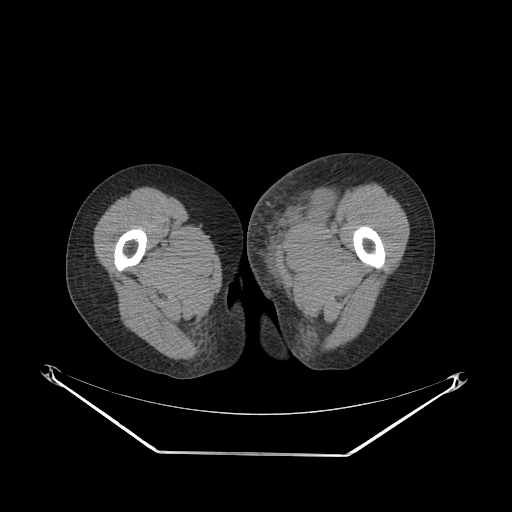
CT of an extremity soft-tissue mass (from a PET/CT study), one axial slice; slice 45 of 267 in the series (ordered by position); 140 kVp; soft-tissue window (W 400 / L 40 HU); 3.75 mm slice thickness; 512 × 512 image matrix, field of view 500 × 500 mm. Female patient. Case-level facts recorded for this patient, not image findings: histological type: leiomyosarcoma; grade: high; site of the primary tumour: groin.
Outlined on this slice (expert contour drawn on MRI and transferred to this co-registered scan by the dataset authors):
- gross tumour volume including surrounding oedema: bounding box [x1, y1, x2, y2] px = [246, 176, 334, 254]
- gross tumour volume (mass): [283, 189, 332, 220]